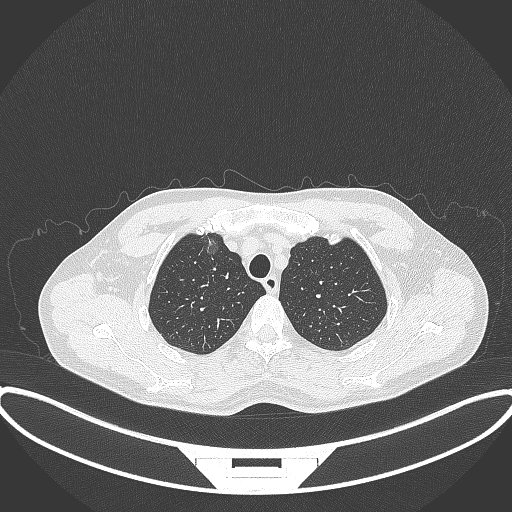
Chest CT, one axial slice. Position 305 of 395 along the scan axis. Reconstruction kernel B70f. Lung window (W 1500 / L -600 HU). 1 mm slice thickness. 512 × 512 image matrix. Male patient, age 60 years. From the clinical record (not read from this slice): clinical TNM (as recorded): T1c N0 M0.
Outlined on this slice (bounding box drawn by a radiologist):
- lung tumour (recorded histology: adenocarcinoma): bounding box [x1, y1, x2, y2] px = [198, 225, 224, 261]